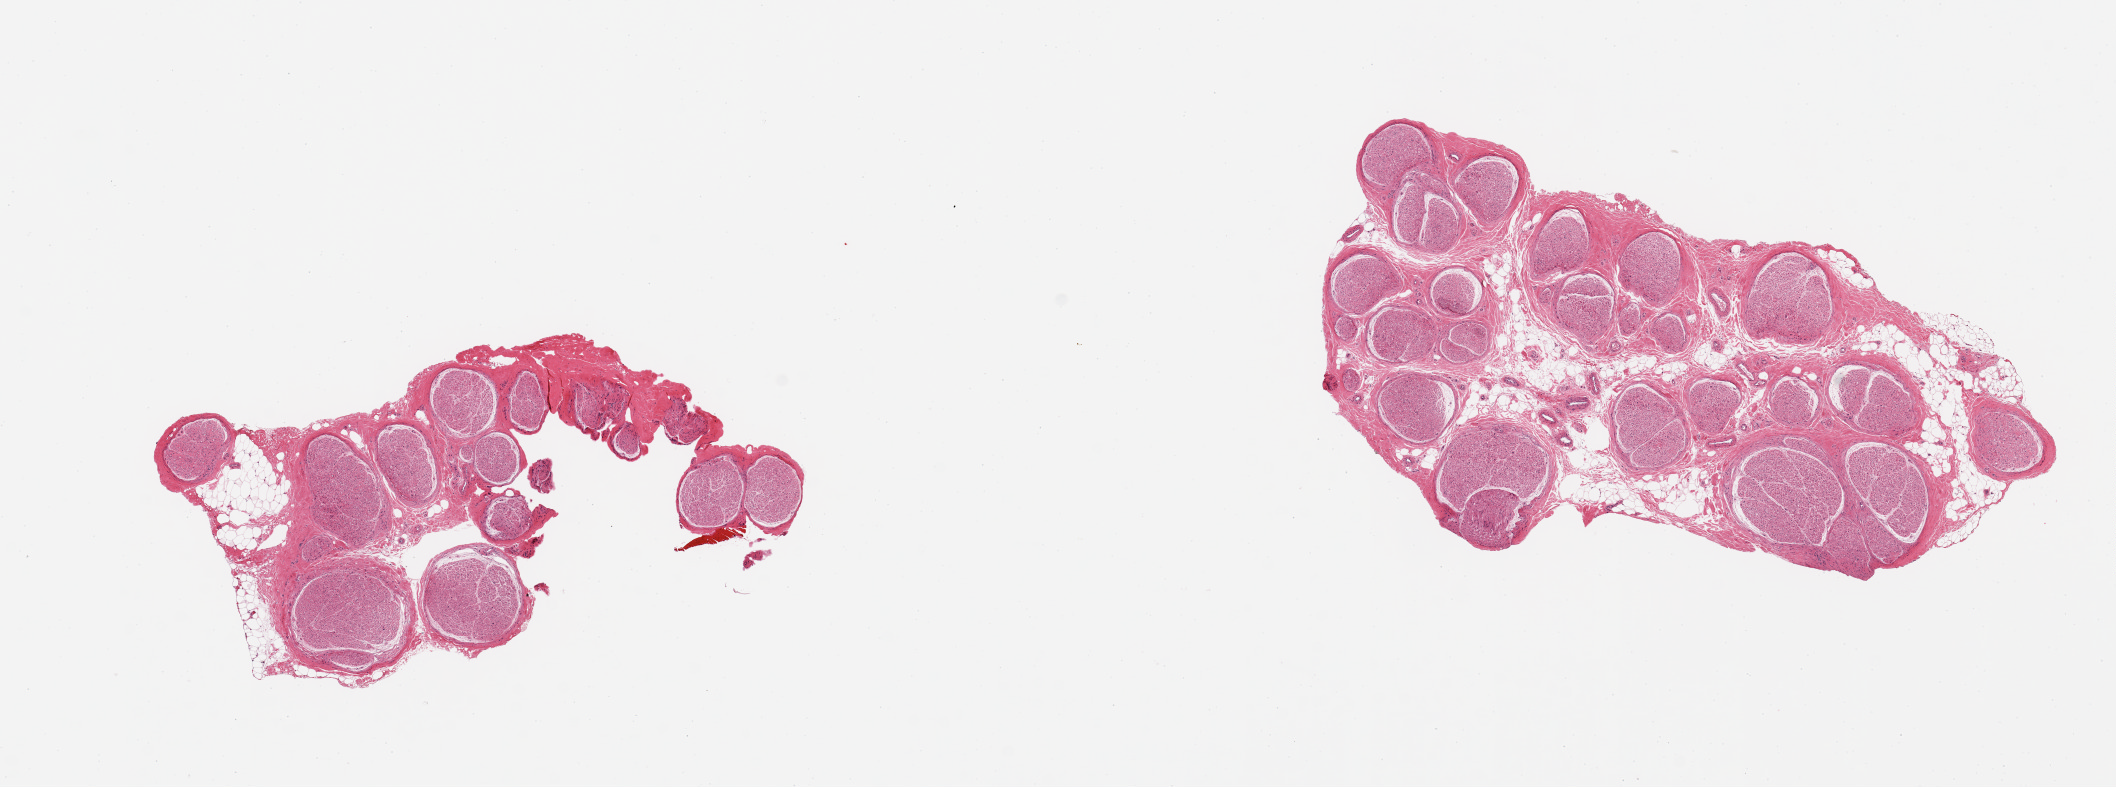
Digitized H&E-stained section — shown as a low-resolution overview of the whole scanned area (about 16.7 x 6.2 mm); PAXgene-fixed, paraffin-embedded tissue; sampled site (target tissue): tibial nerve; donor tissue sample. Donor sex: female.
* pathologist's review note for this sample: 2 pieces 10% internal fat